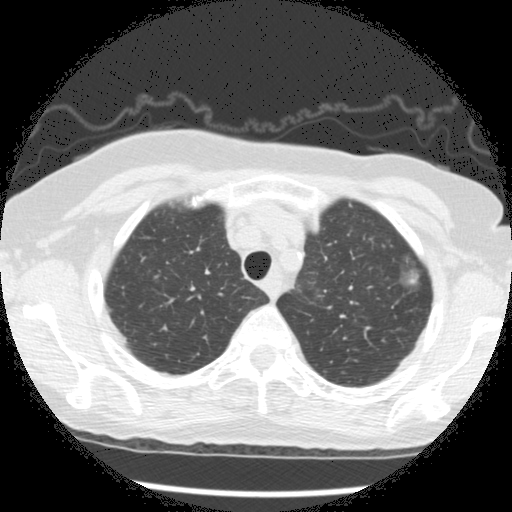
Low-dose screening chest CT, one axial slice. Position 229 of 266 along the scan axis. Reconstruction kernel STANDARD. 120 kVp. Lung window (W 1500 / L -600 HU). 512 × 512 image matrix, field of view 320 × 320 mm.
Structures marked on this image (expert manual segmentation):
- lesion 1 (tumor, upper lobe of left lung): bounding box [x1, y1, x2, y2] px = [408, 273, 418, 285]